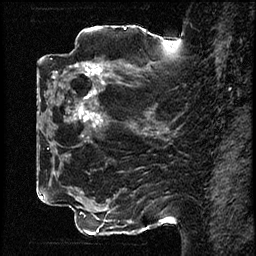
Breast MRI (dynamic contrast-enhanced), one sagittal slice. Position 35 of 78 along the scan axis. Dynamic contrast-enhanced study with each time point stored as its own series, time point 2 of 3 at this slice position (early post-contrast, ordered by acquisition time). 1.5 T. TE 4.2 ms, TR 17.6 ms. 256 × 256 image matrix, field of view 200 × 200 mm. Patient: female, 42 years. Case-level facts recorded for this patient, not image findings: setting: breast cancer imaged before/during neoadjuvant chemotherapy; receptor status: HER2-positive.
Structures marked on this image (semi-automatic segmentation, software-assisted and operator-edited):
- analysis volume of interest (the breast-tissue region the enhancement analysis was run in; not a lesion): bounding box <50,48,131,129> (left, top, right, bottom; pixels)
- tumour enhancement mask (voxels above the 100 % enhancement threshold inside the analysis volume of interest): <74,63,102,121>